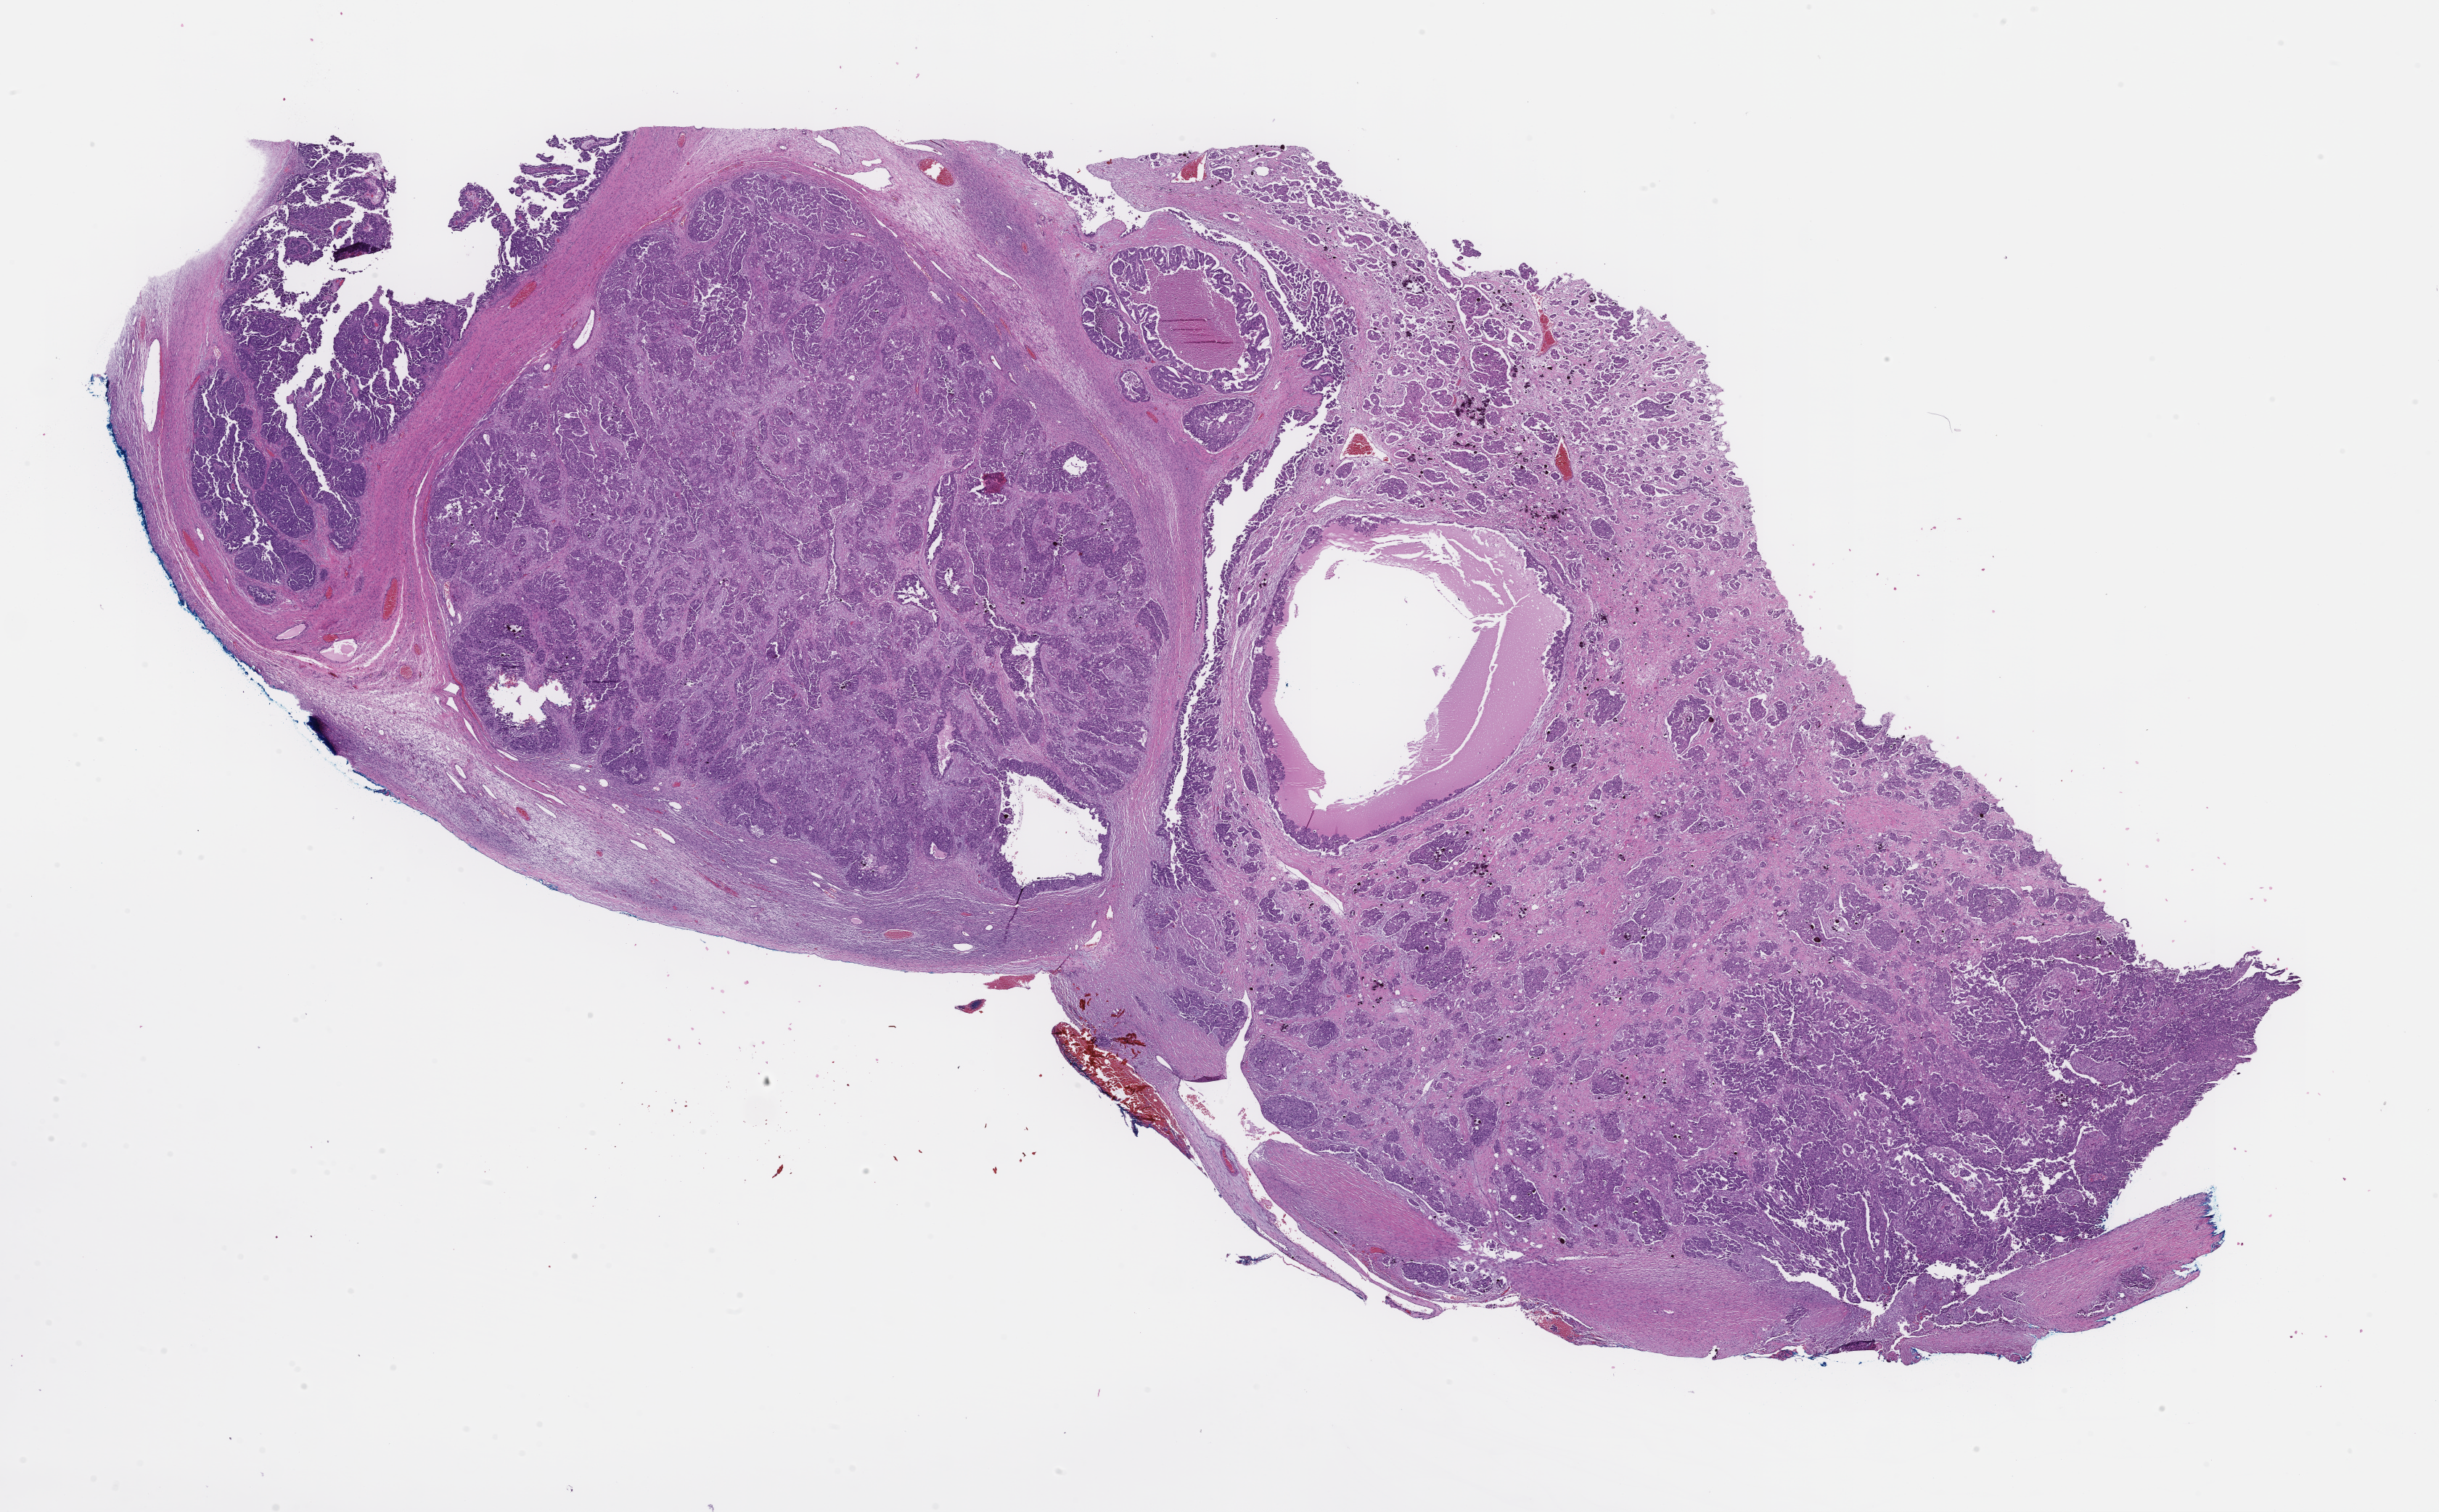
Digitized haematoxylin and eosin-stained section, shown as a low-resolution overview of the whole scanned area (about 27.1 x 16.8 mm). Formalin-fixed paraffin-embedded section. Site: ovary. Archival tissue. Patient: female.
This section: primary tumour tissue. Diagnosis: Ovarian Carcinoma.